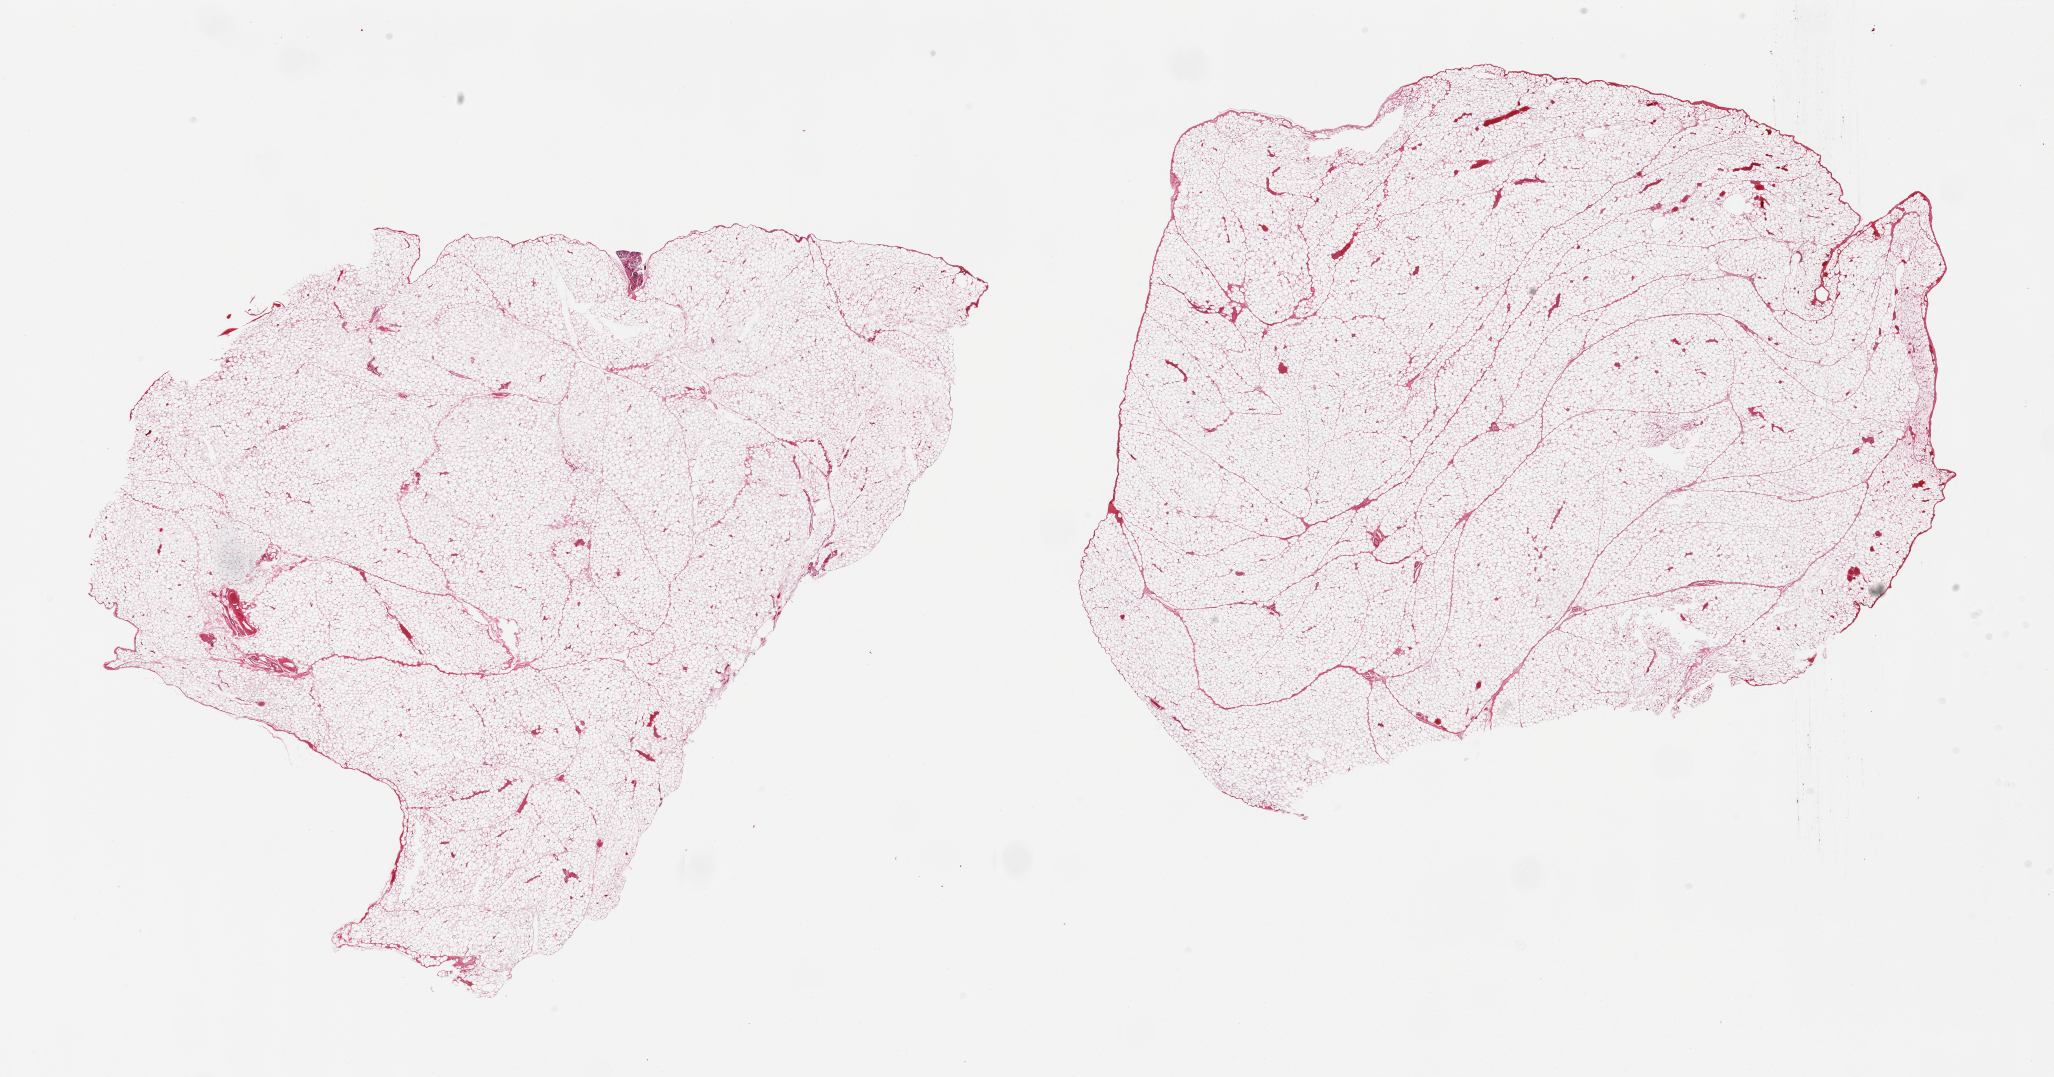
Digitized H&E-stained section, brightfield, shown as a low-resolution overview of the whole scanned area (about 32.5 x 17.0 mm, from a 20x scan); PAXgene-fixed paraffin-embedded (PFPE) section; sampled site (target tissue): omentum; tissue donor sample. Donor: male.
• pathologist's review note for this sample: 2 pieces; oversized, includes fragment of contaminating tissue (seminiferous tubules/concretion)